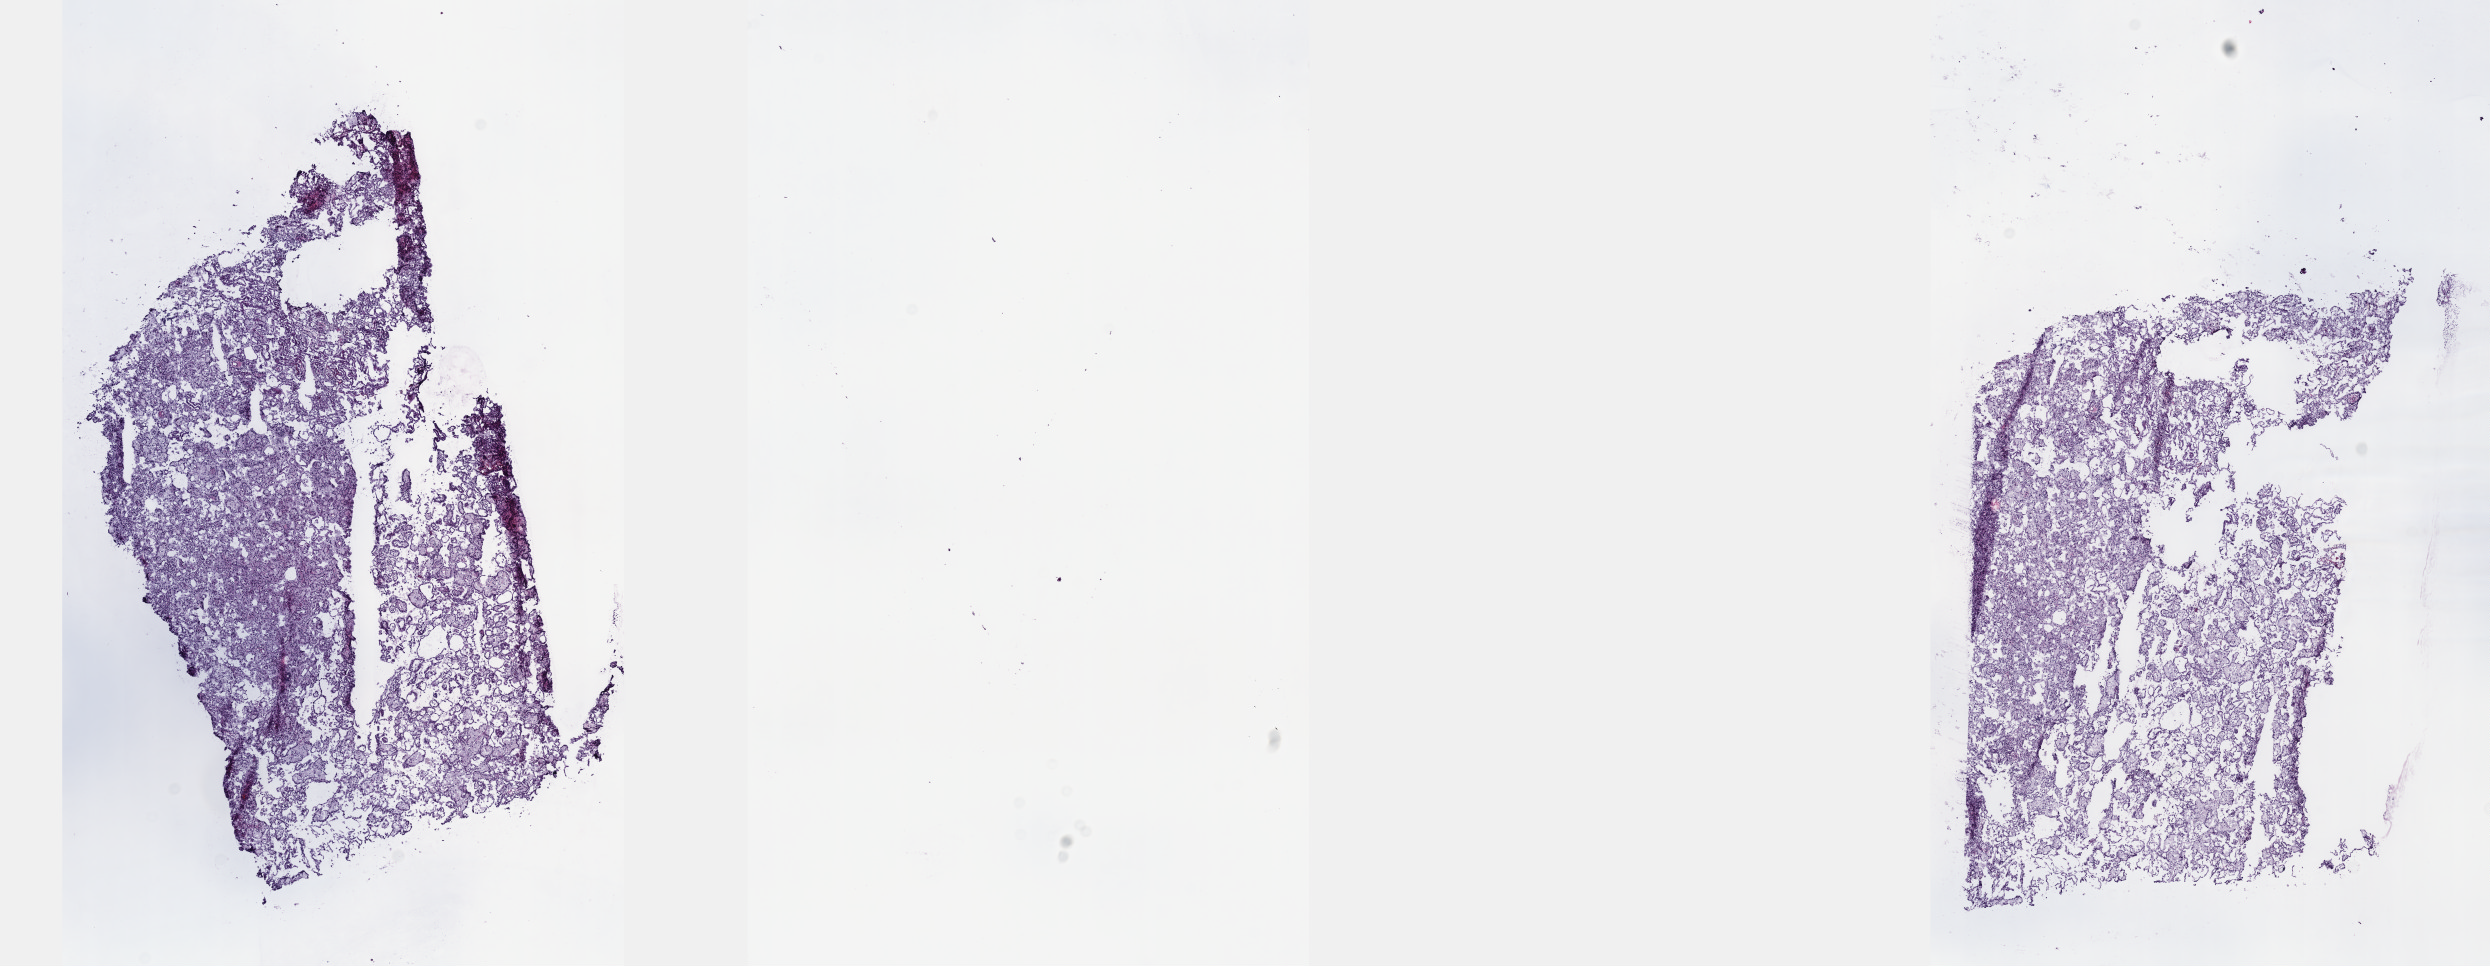
Whole-slide histology image, Hematoxylin and eosin (H&E) stained, a low-resolution overview of the entire scanned area, about 20.1 x 7.8 mm (slide scanned at 40x); frozen section from the top of the tissue portion; sample: primary tumour, kidney. Male, age 57 years at initial diagnosis. Composition of this section per pathologist review: tumour cells 100%, tumour nuclei 80%.
Pathologic diagnosis: Papillary adenocarcinoma, NOS.